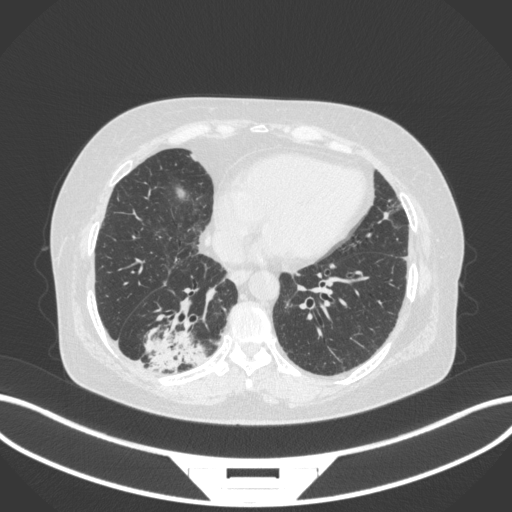
Chest CT, one axial slice. Position 74 of 303 along the scan axis. 120 kVp. Lung window (W 1500 / L -600 HU). 1 mm slice thickness. 512 × 512 image matrix. Patient: female, 65 years. From the clinical record (not read from this slice): clinical TNM (as recorded): T2b N1 M0; histopathological grade: G1.
Annotated regions visible in this slice (rectangle marked by the reading radiologist):
- lung tumour (recorded histology: adenocarcinoma): bounding box [x1, y1, x2, y2] px = [138, 312, 209, 376]